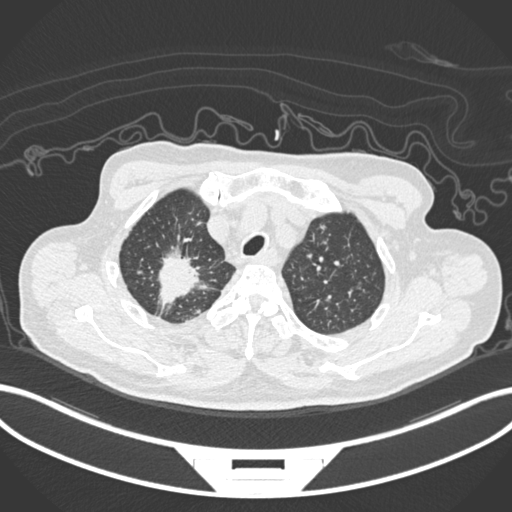
Chest CT, one axial slice; position 181 of 207 along the scan axis; 120 kVp; lung window (W 1500 / L -600 HU); 512 × 512 image matrix, field of view 400 × 400 mm. Patient: male, 69 years. From the clinical record (not read from this slice): clinical TNM (as recorded): T1c N1 M1.
Outlined on this slice (rectangle marked by the reading radiologist):
- lung tumour (recorded histology: adenocarcinoma): box from (x=151, y=234) to (x=216, y=314) px